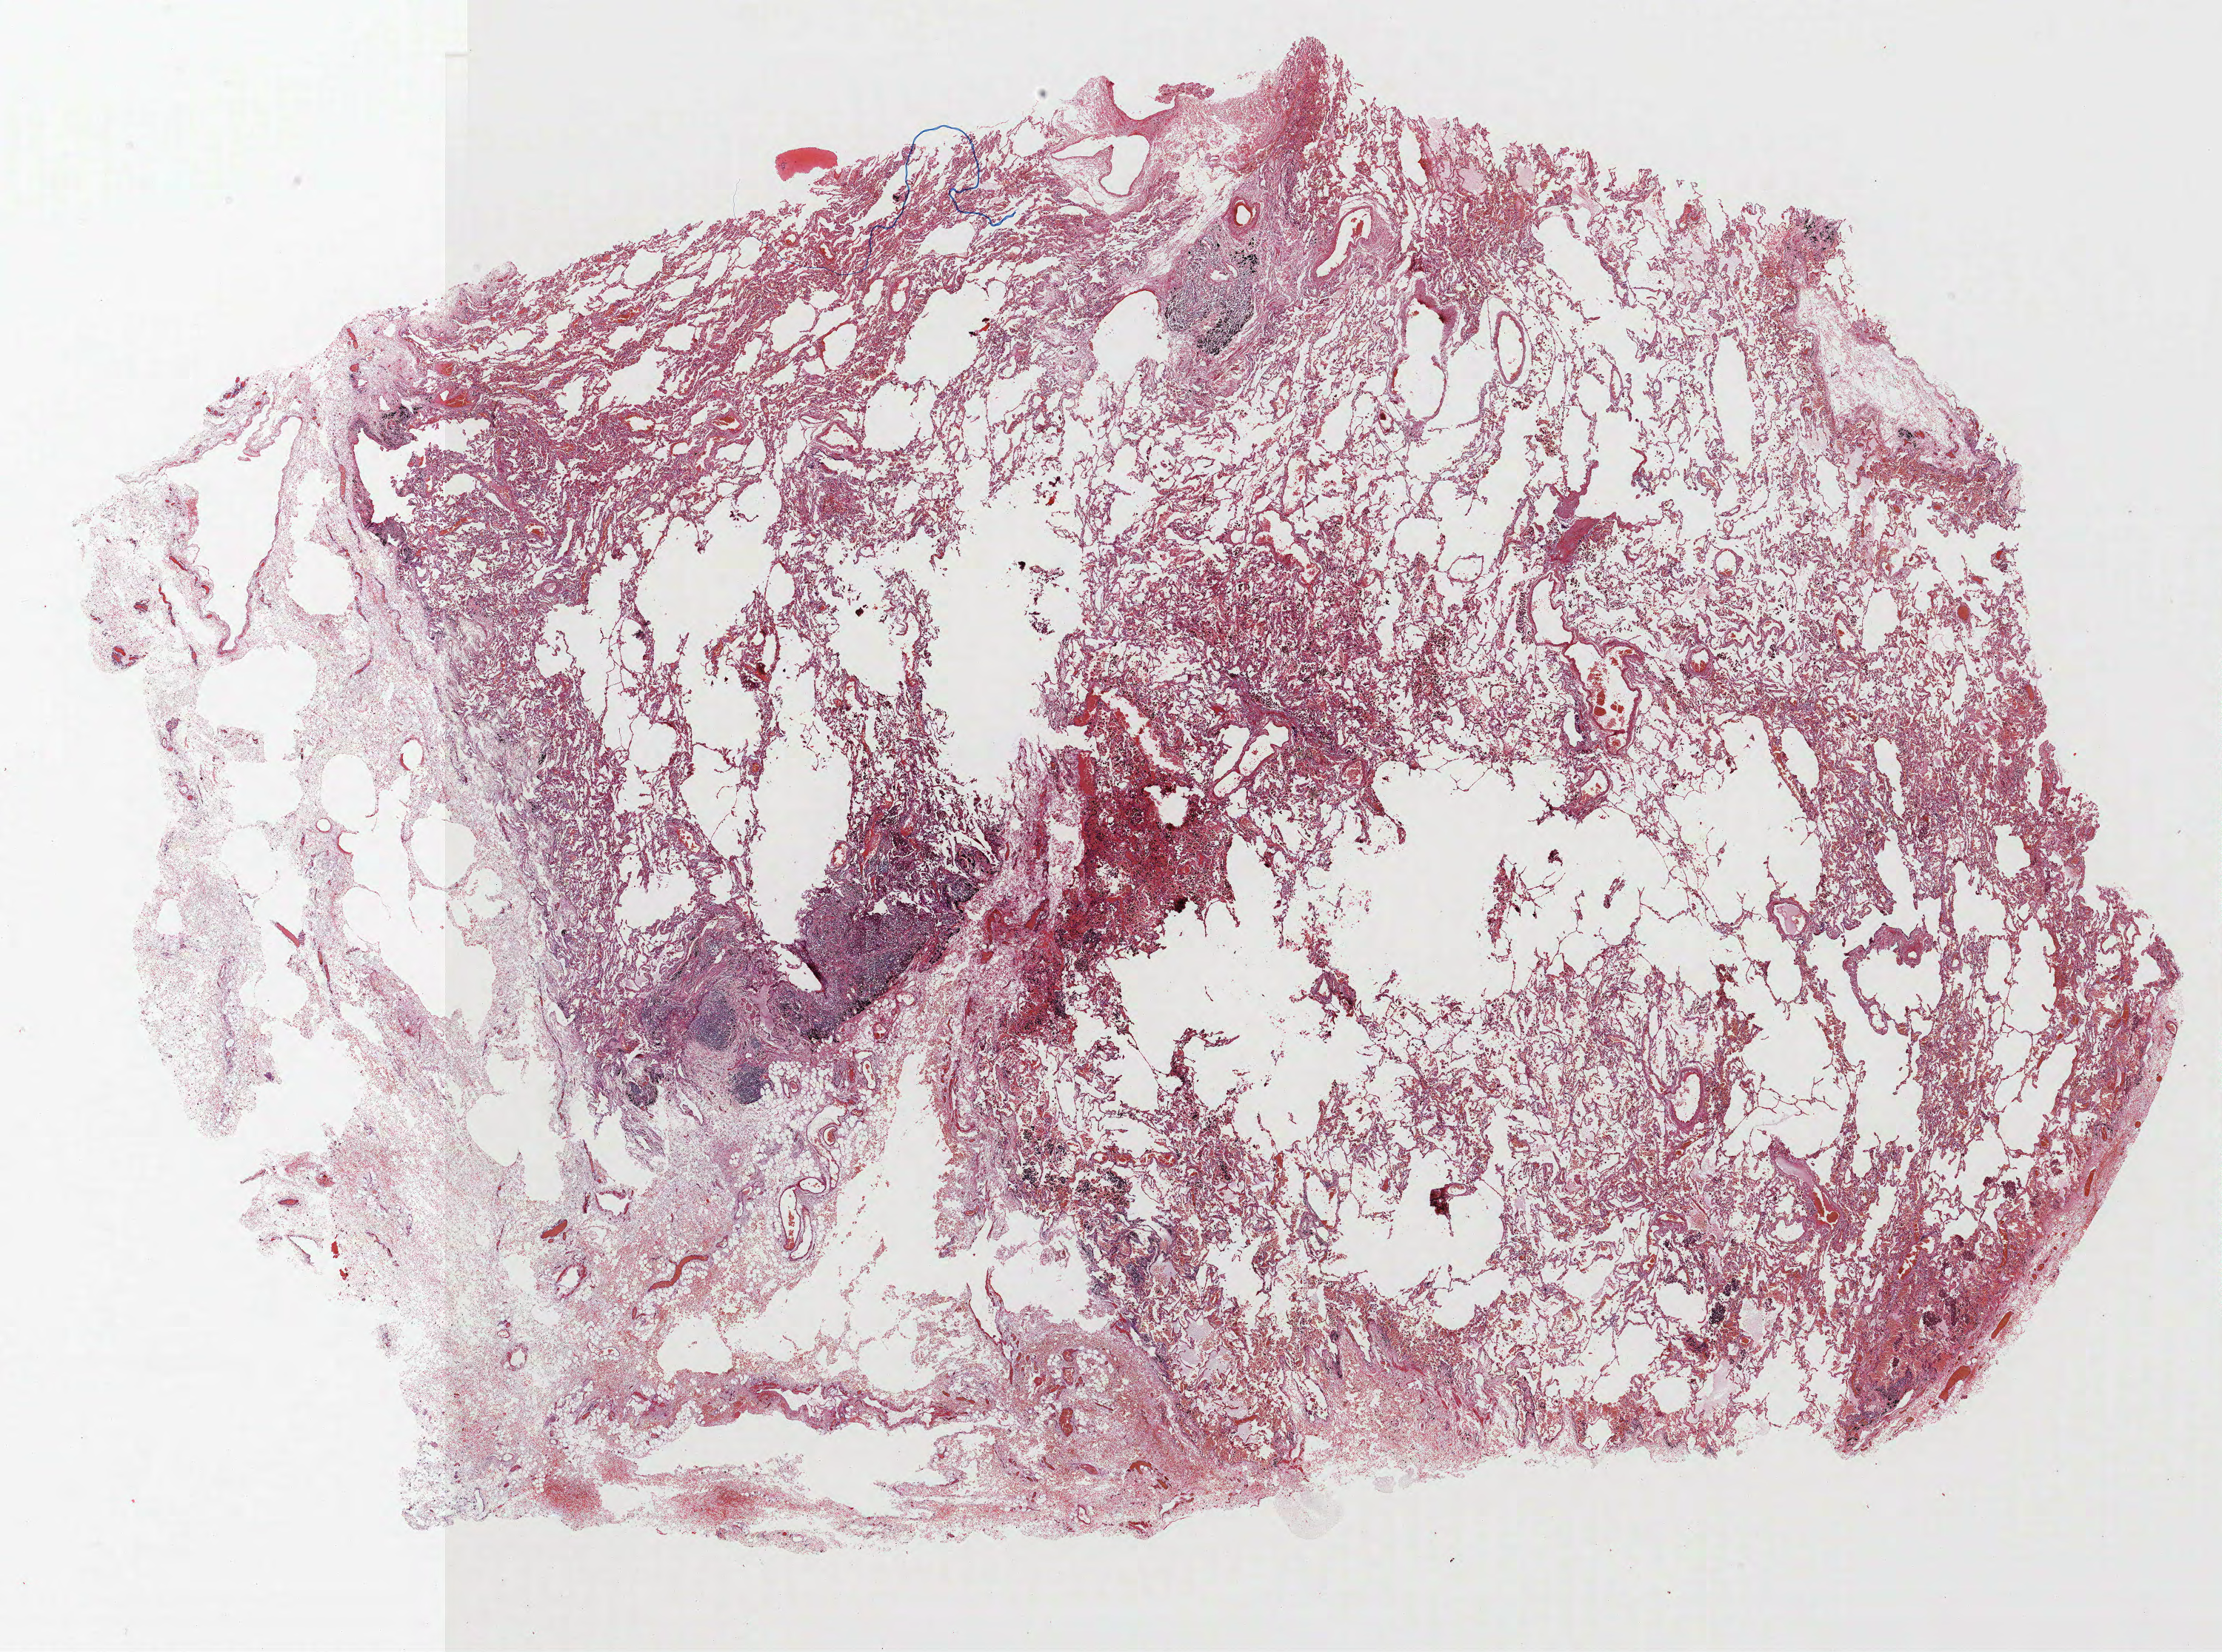
Whole-slide histology image, H&E-stained, whole scanned area (about 24.0 x 17.9 mm, acquisition: 40x scan) shown as a low-resolution overview; formalin-fixed paraffin-embedded (FFPE) section; lung. Male patient, aged 63 at enrolment. Current smoker at enrolment. Grade: moderately differentiated (G2).
• tumour size (pathology): 15 mm
• stage (AJCC 6th edition): IA
• primary tumour location (clinical record): left lower lobe
• participant's lung-cancer diagnosis: Adenocarcinoma, NOS
• ICD-O-3 topography: lower lobe of lung (C34.3)